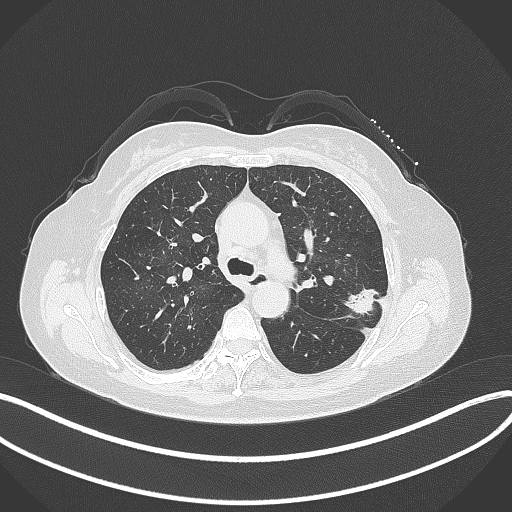
Chest CT, one axial slice; slice 217 of 319 in the series (ordered by position); reconstruction kernel B70f; 120 kVp; lung window (W 1500 / L -600 HU); 512 × 512 image matrix. Patient: female, 60 years. From the clinical record (not read from this slice): clinical TNM (as recorded): T1c N0 M0.
Outlined on this slice (bounding box drawn by a radiologist):
- lung tumour (recorded histology: adenocarcinoma): box from (x=345, y=282) to (x=382, y=317) px